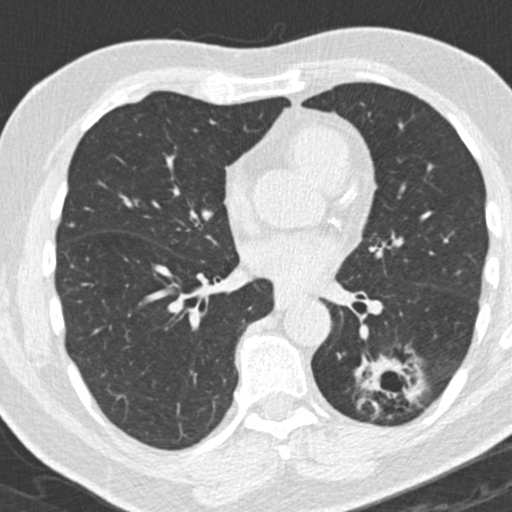
Low-dose screening chest CT, one axial slice. Position 93 of 180 along the scan axis. 120 kVp. Lung window (W 1500 / L -600 HU). 512 × 512 image matrix, field of view 300 × 300 mm.
Structures marked on this image (expert manual segmentation):
- lesion 1 (tumor, lower lobe of left lung): box from (x=363, y=358) to (x=422, y=400) px